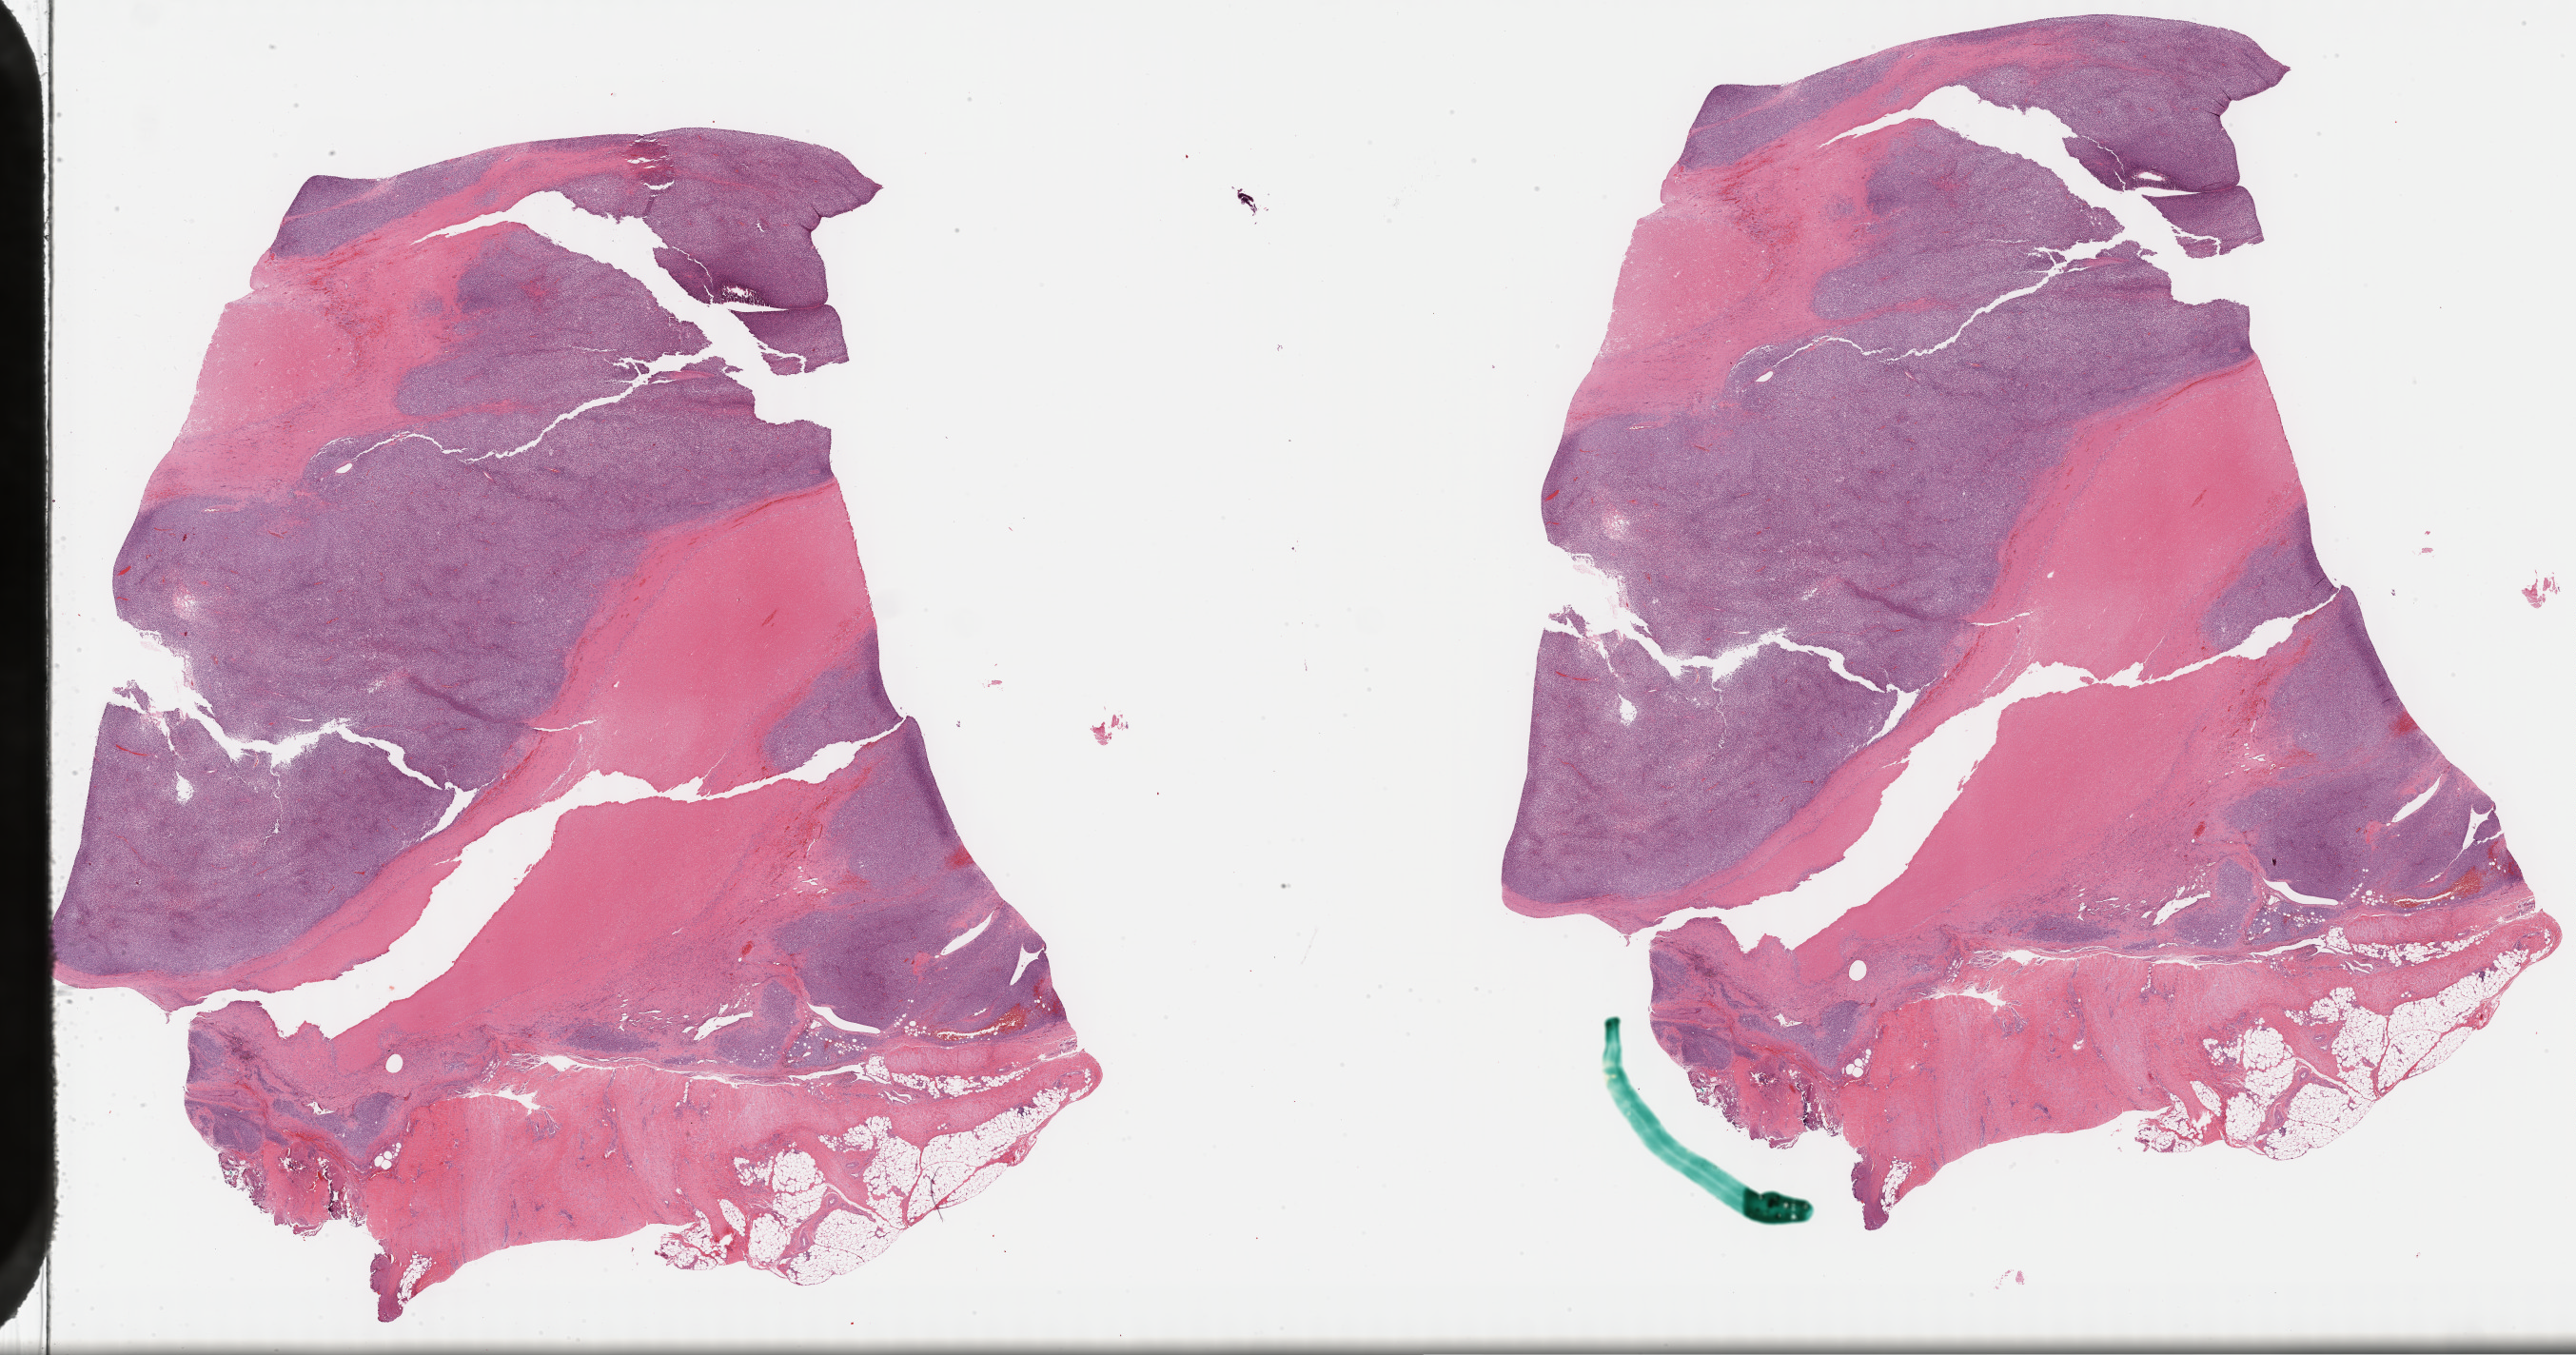
Digitized Hematoxylin and eosin (H&E) stained tissue section (whole slide), a low-resolution overview of the entire scanned area, about 43.8 x 23.0 mm, FFPE section, primary tumour sample from the connective, subcutaneous and other soft tissues. Male, age 27 years at initial diagnosis.
* histologic diagnosis: Synovial sarcoma, spindle cell (connective, subcutaneous and other soft tissues of lower limb and hip)